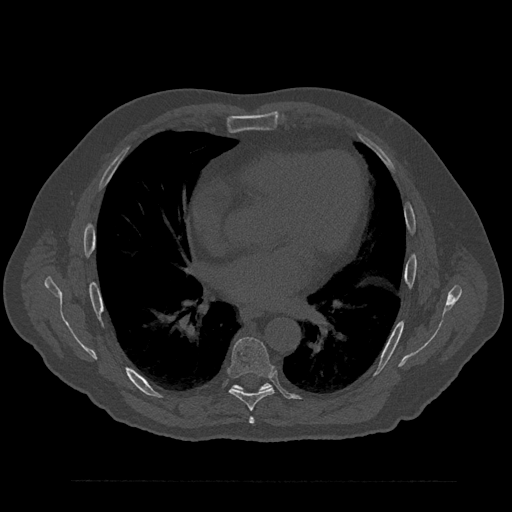
CT including the spine, one axial slice; slice 495 of 797 in the series (ordered by position); 120 kVp; bone window (W 1800 / L 400 HU); 0.5 mm slice thickness; 512 × 512 image matrix, field of view 430 × 430 mm. Male patient, age 61 years. From the clinical record (not read from this slice): primary cancer: prostate.
Annotated regions visible in this slice (semi-automatic segmentation, software-assisted and operator-edited):
- T6 vertebra: bounding box [x1, y1, x2, y2] px = [249, 417, 255, 424]
- T7 vertebra: [228, 337, 274, 411]
- T8 vertebra: [232, 383, 271, 392]